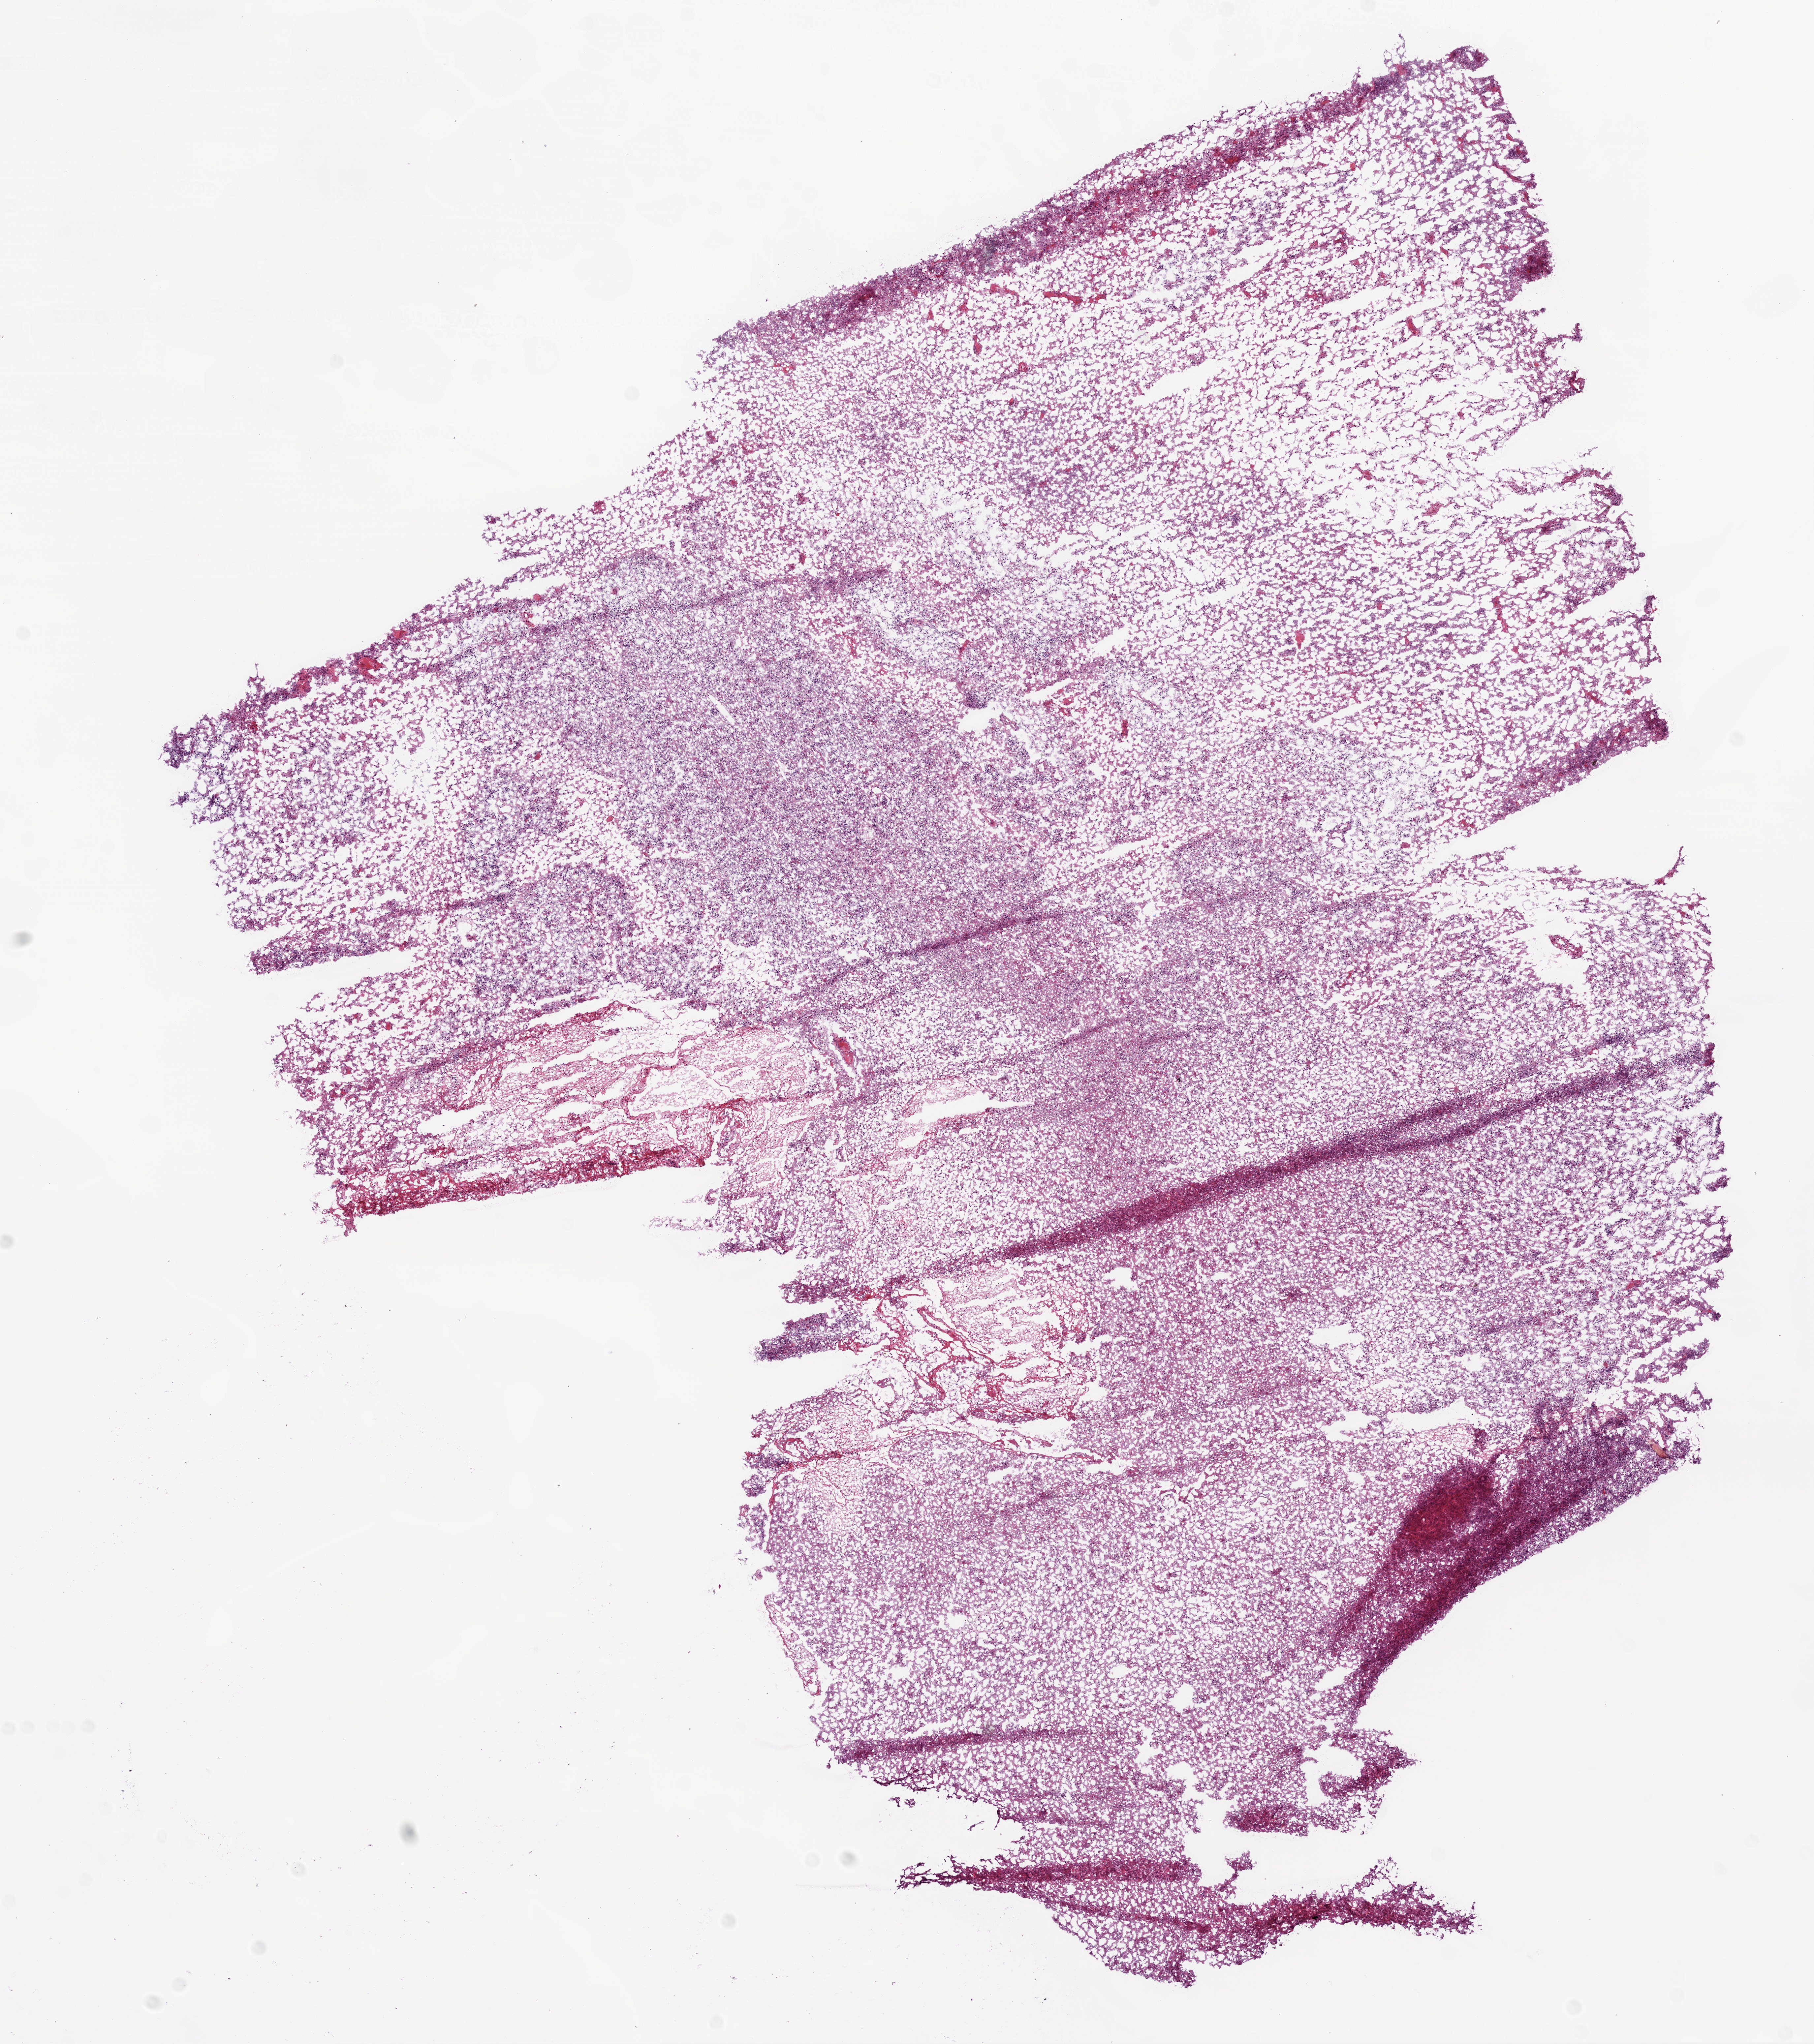
Whole-slide histology image, Hematoxylin and eosin (H&E) stained, shown as a low-resolution overview of the whole scanned area (about 11.0 x 12.4 mm), frozen section from the bottom of the tissue portion, primary tumour sample from the brain. Female, age 40 years at initial diagnosis. Pathologist review of this section (percent, as recorded): tumour cells 70%, tumour nuclei 90%, normal cells 0%, stromal cells 5%, necrosis 25%. Inflammatory infiltration, as recorded: lymphocyte infiltration 100%.
* diagnosis: Glioblastoma